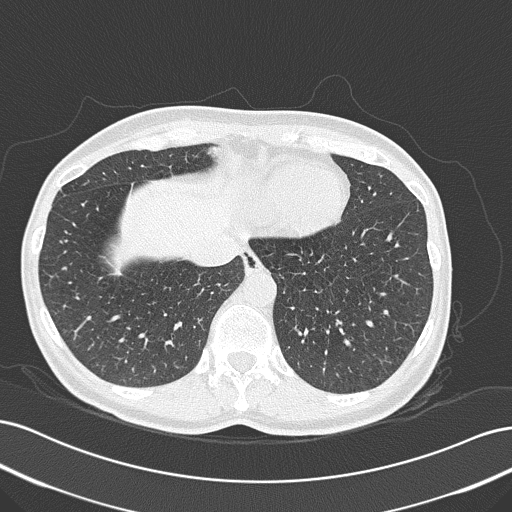
Chest CT (low-dose screening protocol), one axial image; baseline screening round; lung window (W 1500 / L -600 HU); lung (sharp) reconstruction kernel (B50f); 120 kVp; 512 × 512 image matrix. Female participant, aged 55 years at enrolment. Current smoker at enrolment.
• Expert-annotated lung lesion, bounding box [x1, y1, x2, y2] px = [321, 307, 359, 344].
• The exam's reader record, not a measurement of the box and not confirmed to be the same lesion: non-calcified nodule or mass ≥4 mm, right upper lobe, 14 × 7 mm, spiculated (stellate) margins, ground glass attenuation.
• Note: the box lies in the patient's left hemithorax on this image, whereas the reader's record names the right lung; they may be different findings.
• Official screen result: positive, change unspecified: nodule(s) >= 4 mm or enlarging nodule(s), mass(es), or other non-specific abnormalities suspicious for lung cancer.
• Participant outcome: lung cancer diagnosed 1065 days after this screen (after the third annual screen) — adenocarcinoma, NOS, left lower lobe, well differentiated (G1), stage IA (AJCC 6th edition), 11 mm at pathology.